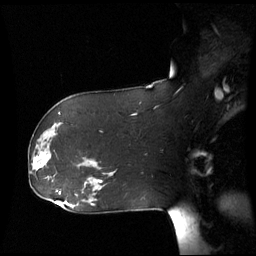
Breast MRI (dynamic contrast-enhanced), one sagittal slice. Position 37 of 60 along the scan axis. Dynamic contrast-enhanced series, image 2 of 3 at this slice position (ordered by acquisition). 1.5 T. TE 4.2 ms, TR 8.9 ms. 2.7 mm slice thickness. 256 × 256 image matrix, field of view 280 × 280 mm. Patient: female, 61 years. Case-level facts recorded for this patient, not image findings: setting: breast cancer imaged before/during neoadjuvant chemotherapy; receptor status: HR-positive, HER2-negative.
Structures marked on this image (semi-automatically segmented with operator editing):
- analysis volume of interest (the breast-tissue region the enhancement analysis was run in; not a lesion): bounding box (x1, y1, x2, y2) in pixels: (28, 142, 55, 177)
- tumour enhancement mask (voxels above the 70 % enhancement threshold inside the analysis volume of interest): (34, 152, 49, 169)